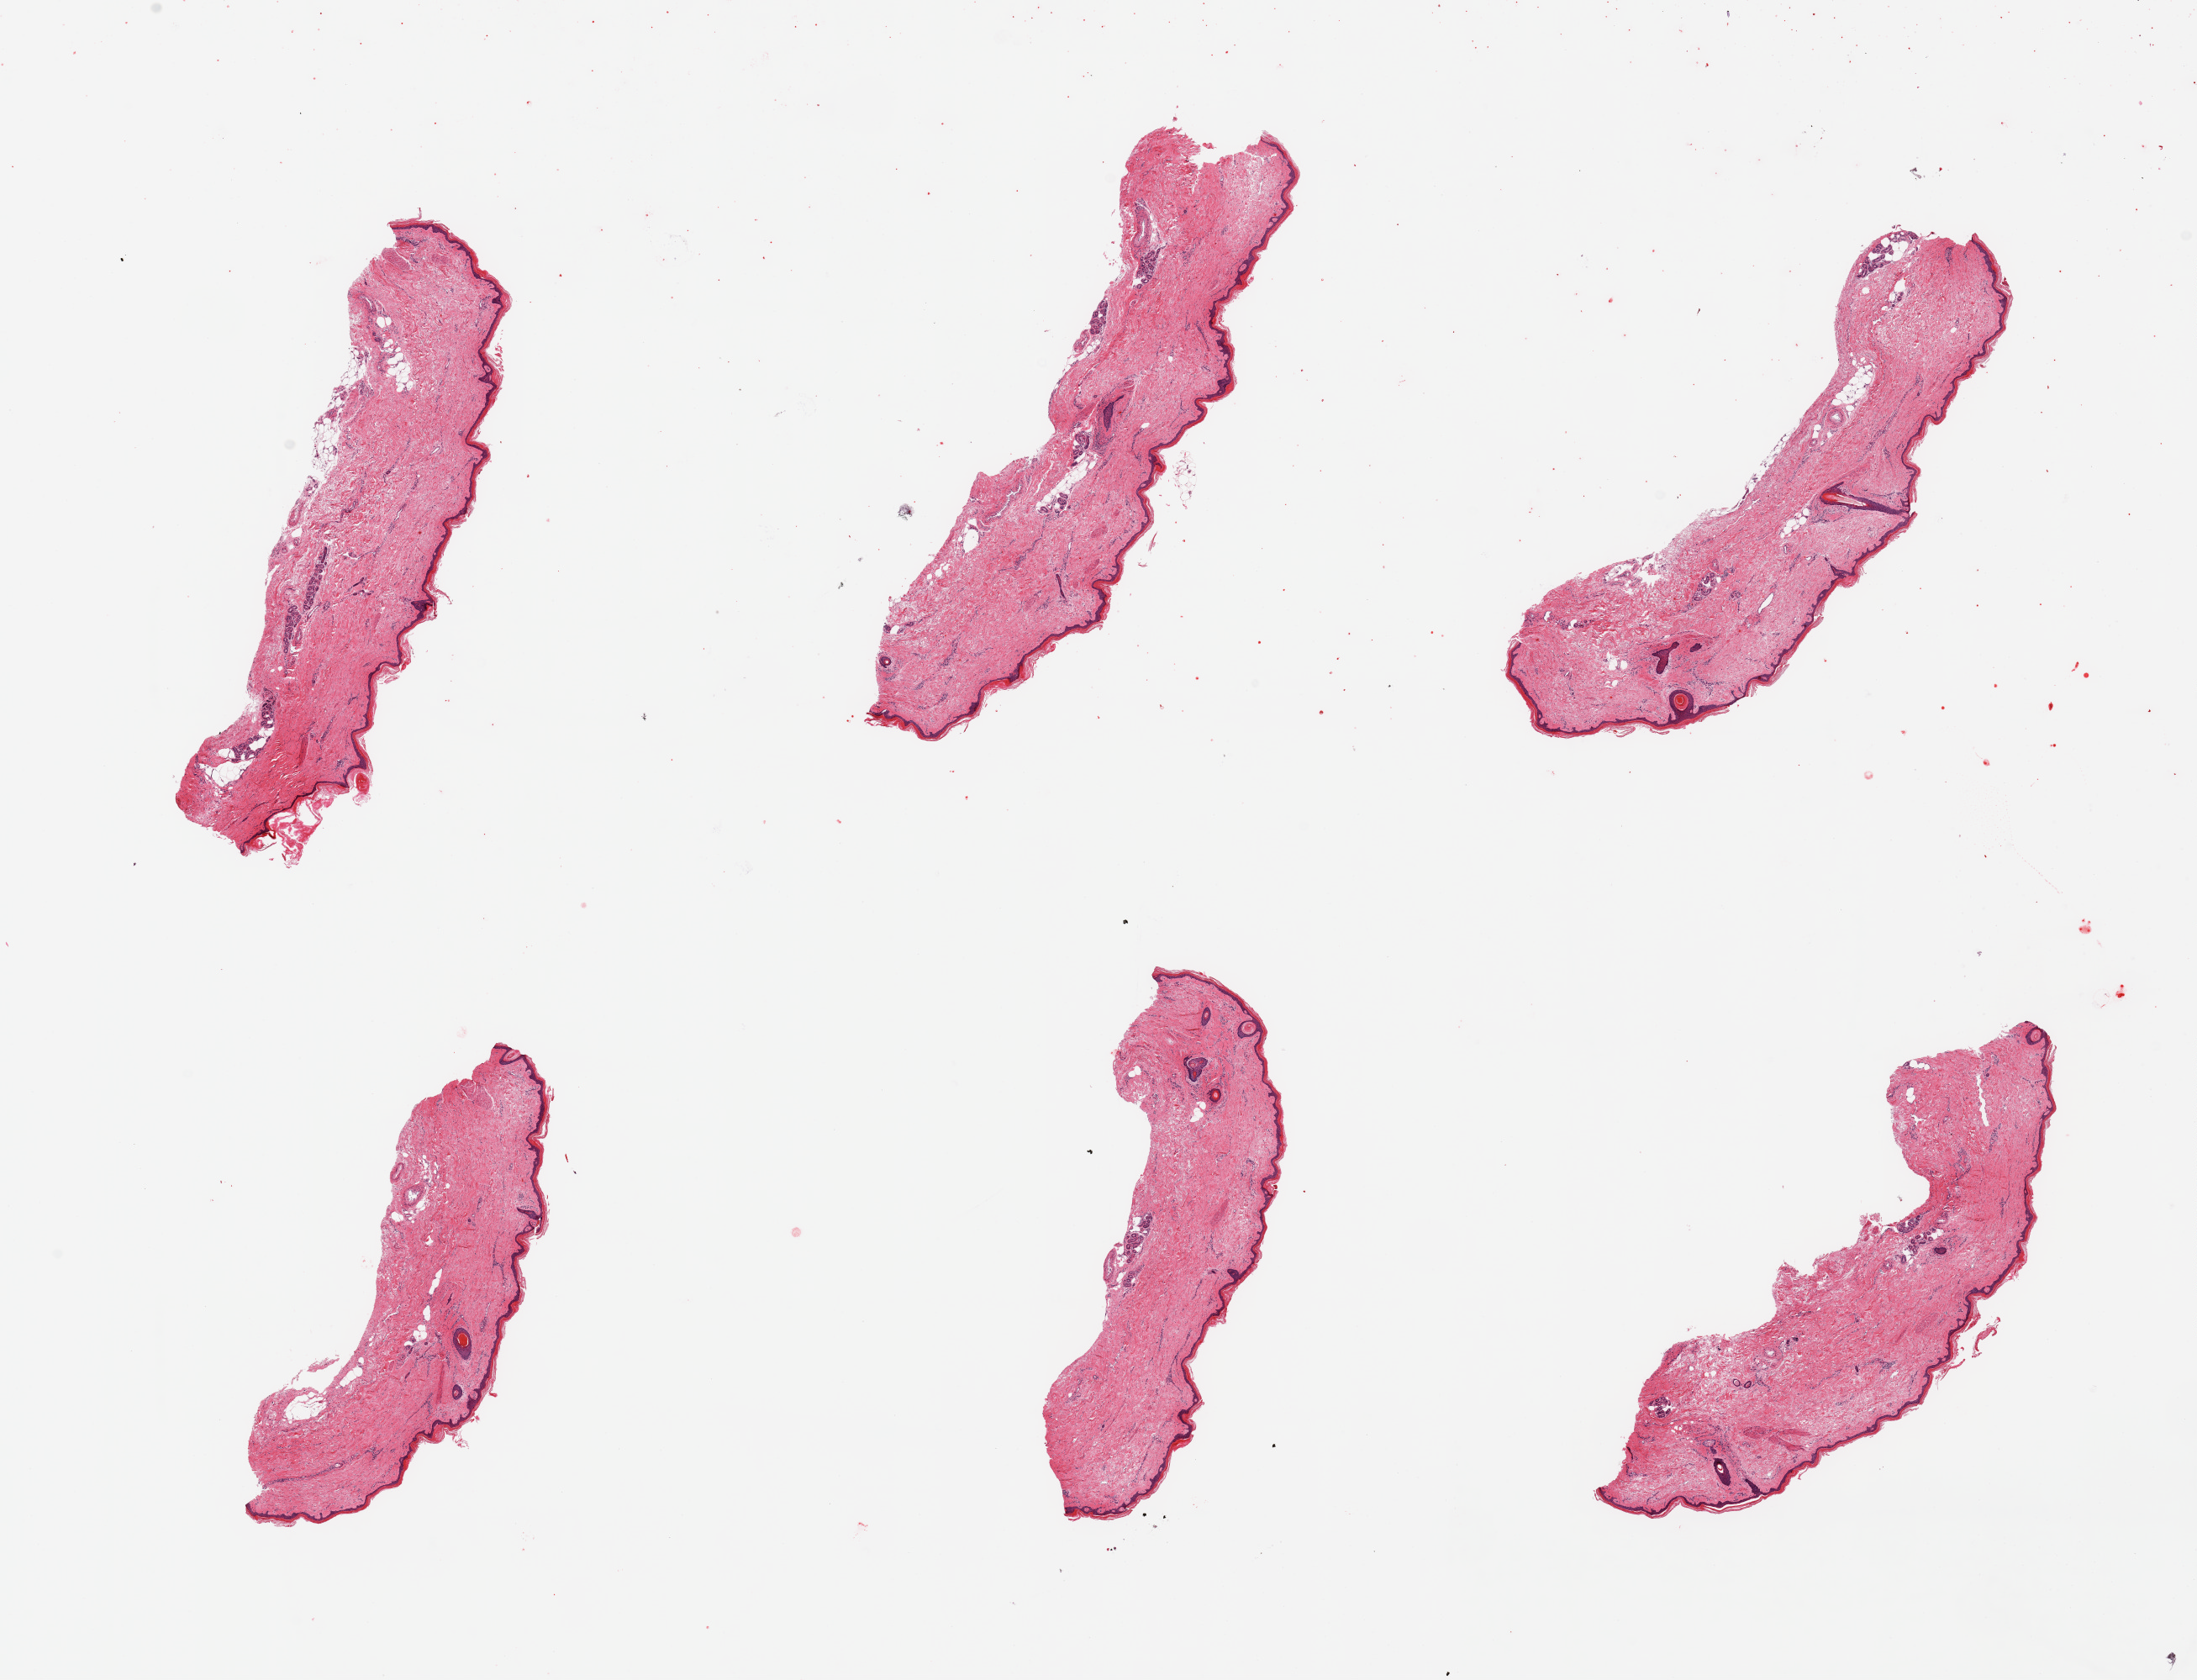
Digitized hematoxylin and eosin (H&E)-stained section, brightfield — a low-resolution overview of the entire scanned area, about 20.7 x 15.8 mm, PAXgene-fixed, paraffin-embedded tissue, sampled site (target tissue): skin of lower leg, donor tissue sample. Female donor.
Review note (as recorded): 6 pieces; well trimmed; dermal fat <5%.